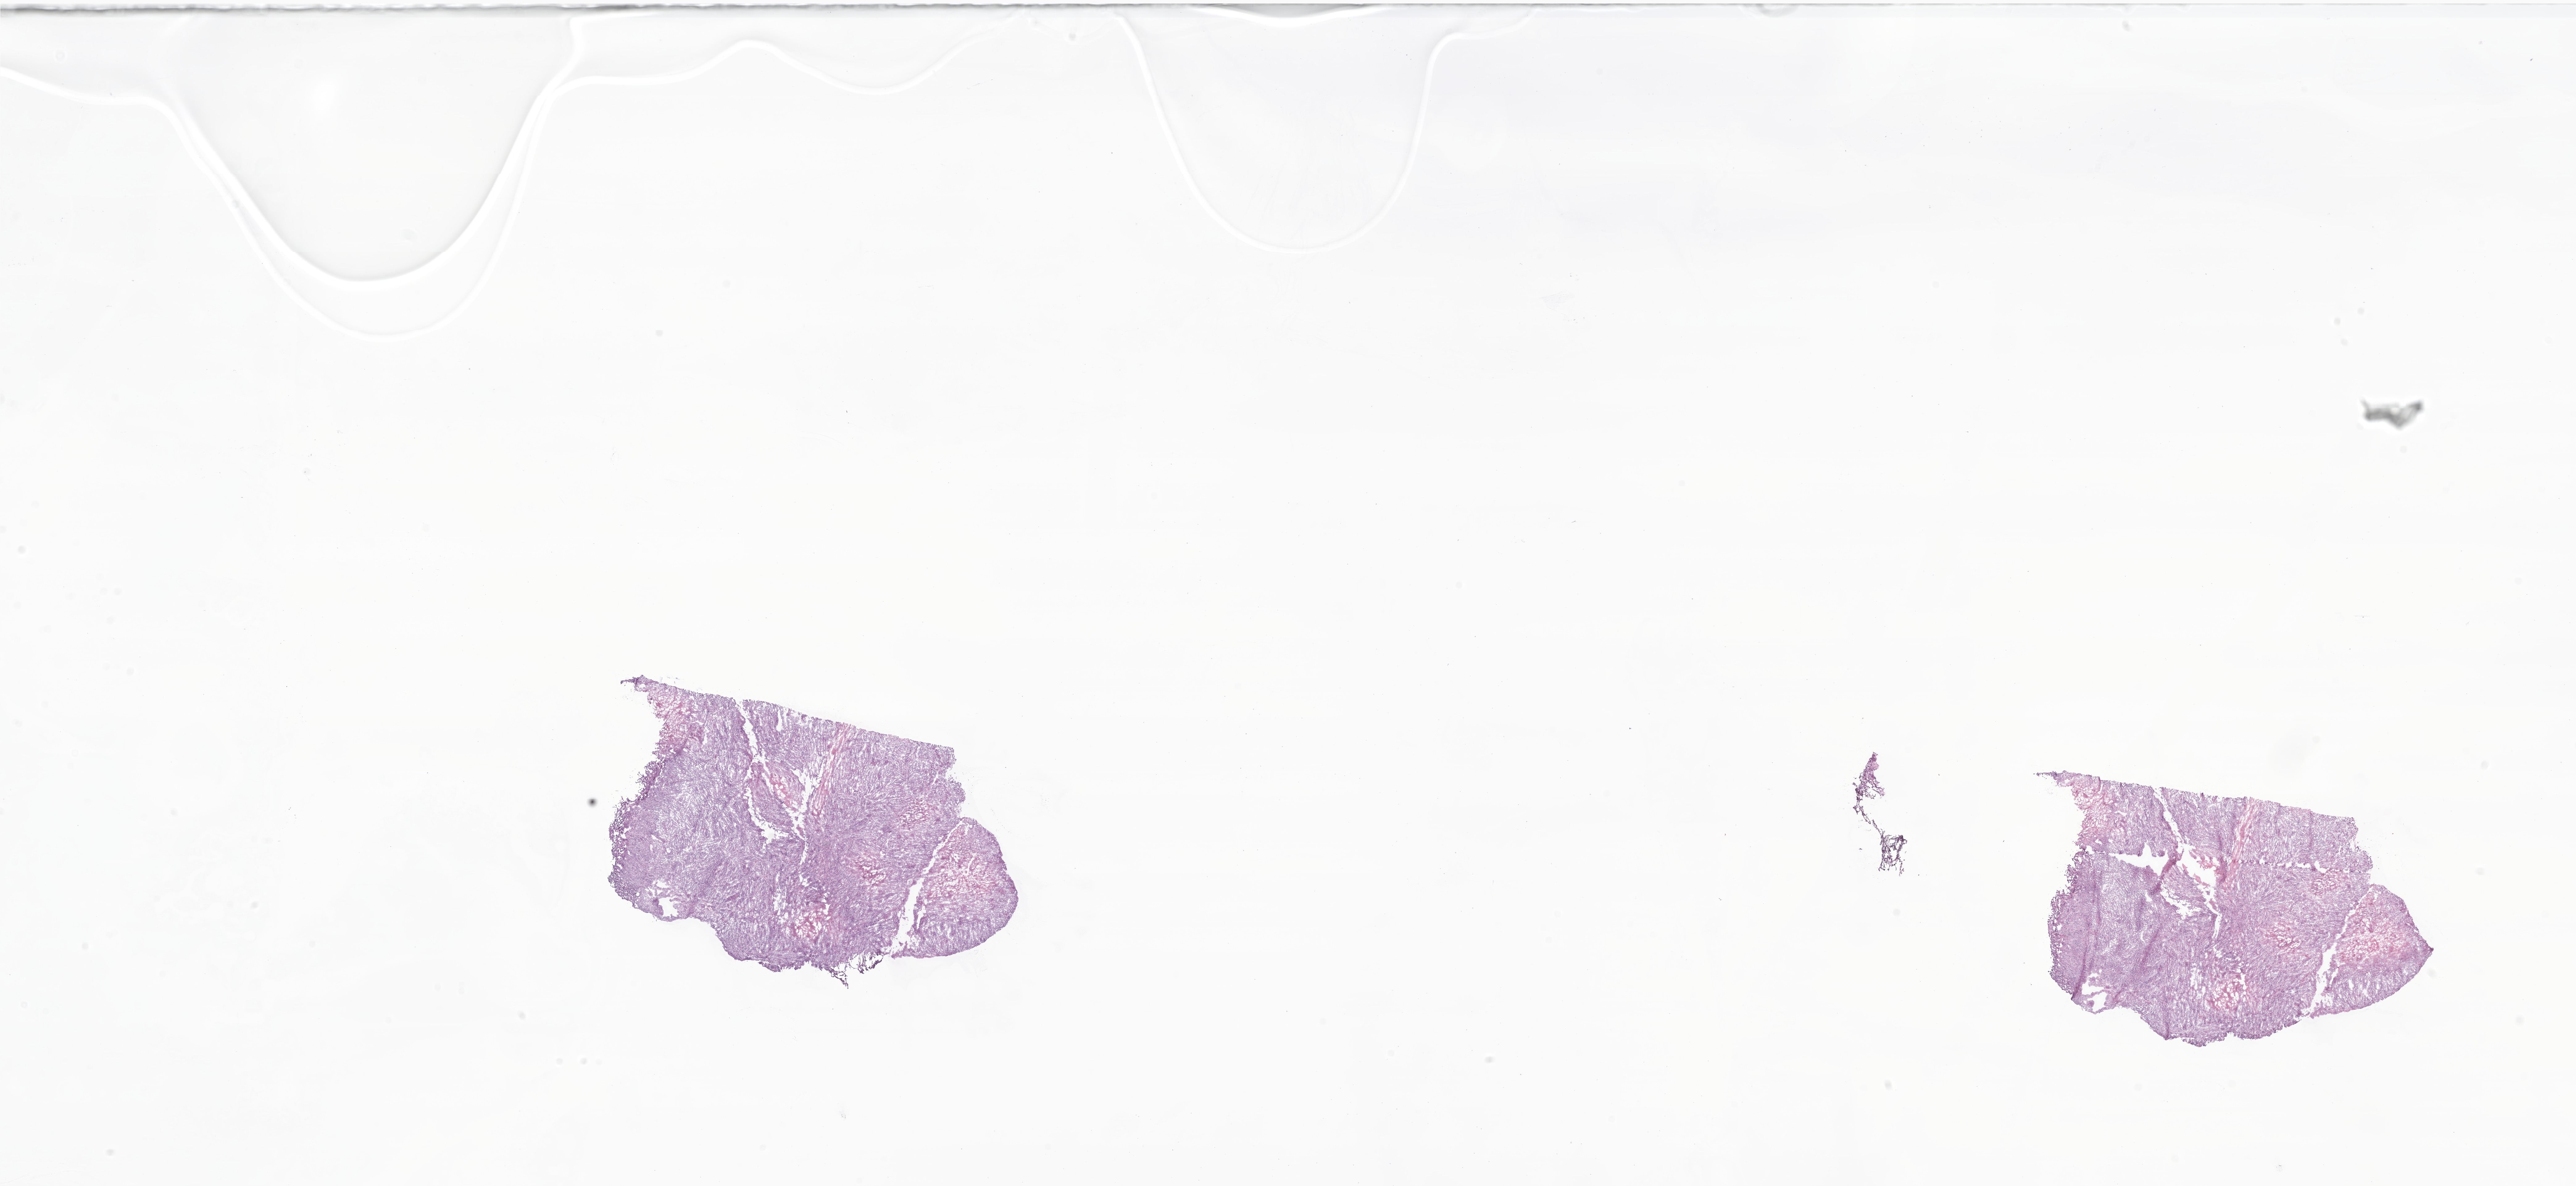
Digitized haematoxylin and eosin-stained section of tumor tissue from the head and neck lymph node — whole scanned area (about 35.2 x 16.2 mm) shown as a low-resolution overview. Frozen section (OCT-embedded). Male patient, age 185 months (15 years 5 months).
Recorded diagnosis: Squamous cell carcinoma, metastatic, NOS.